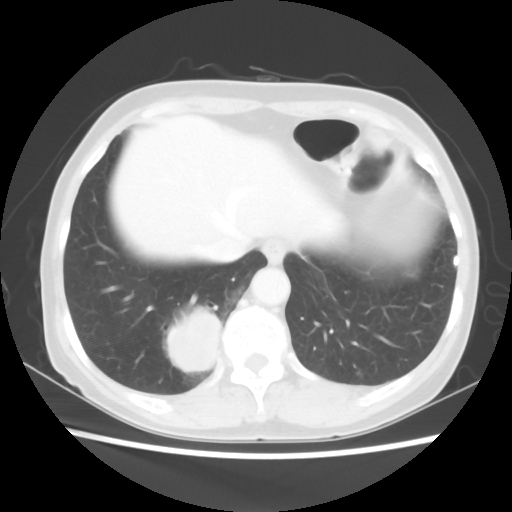
Chest CT, one axial slice; slice 12 of 56 in the series (ordered by position); reconstruction kernel STANDARD; lung window (W 1500 / L -600 HU); 5 mm slice thickness; 512 × 512 image matrix, field of view 332 × 332 mm. Female patient, age 66 years. Case-level facts recorded for this patient, not image findings: clinical TNM (as recorded): T2 N3 M0.
Outlined on this slice (rectangle marked by the reading radiologist):
- lung tumour (recorded histology: small cell carcinoma): bounding box <163,309,240,380> (left, top, right, bottom; pixels)